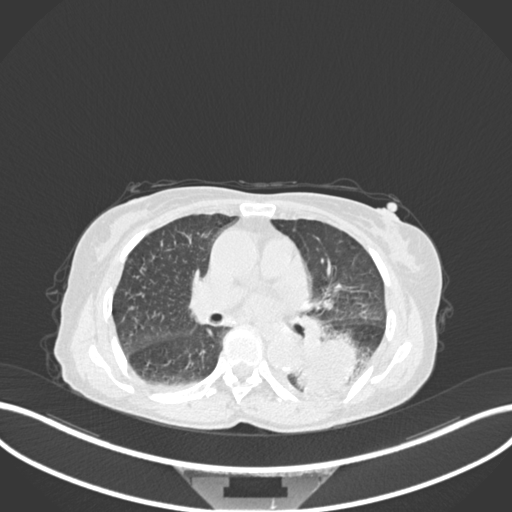
Chest CT, one axial slice. Slice 92 of 233 in the series (ordered by position). Reconstruction kernel B30f. 120 kVp. Lung window (W 1500 / L -600 HU). 1 mm slice thickness. 512 × 512 image matrix, field of view 400 × 400 mm. Female patient, age 78 years. Case-level facts recorded for this patient, not image findings: clinical TNM (as recorded): T3 N0 M1.
Outlined on this slice (rectangle marked by the reading radiologist):
- lung tumour (recorded histology: squamous cell carcinoma): bounding box (x1, y1, x2, y2) in pixels: (294, 331, 363, 397)